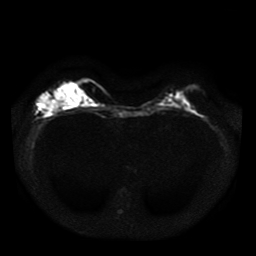
Breast MRI, one axial slice; position 13 of 41 along the scan axis; diffusion-weighted series; image 2 of 4 stored at this slice position (different b-values; order by instance number); 1.5 T; 5 mm slice thickness; 256 × 256 image matrix, field of view 330 × 330 mm. Female patient.
Structures marked on this image (manually delineated by an expert):
- tumour on diffusion-weighted imaging: bounding box (x1, y1, x2, y2) in pixels: (45, 91, 62, 112)